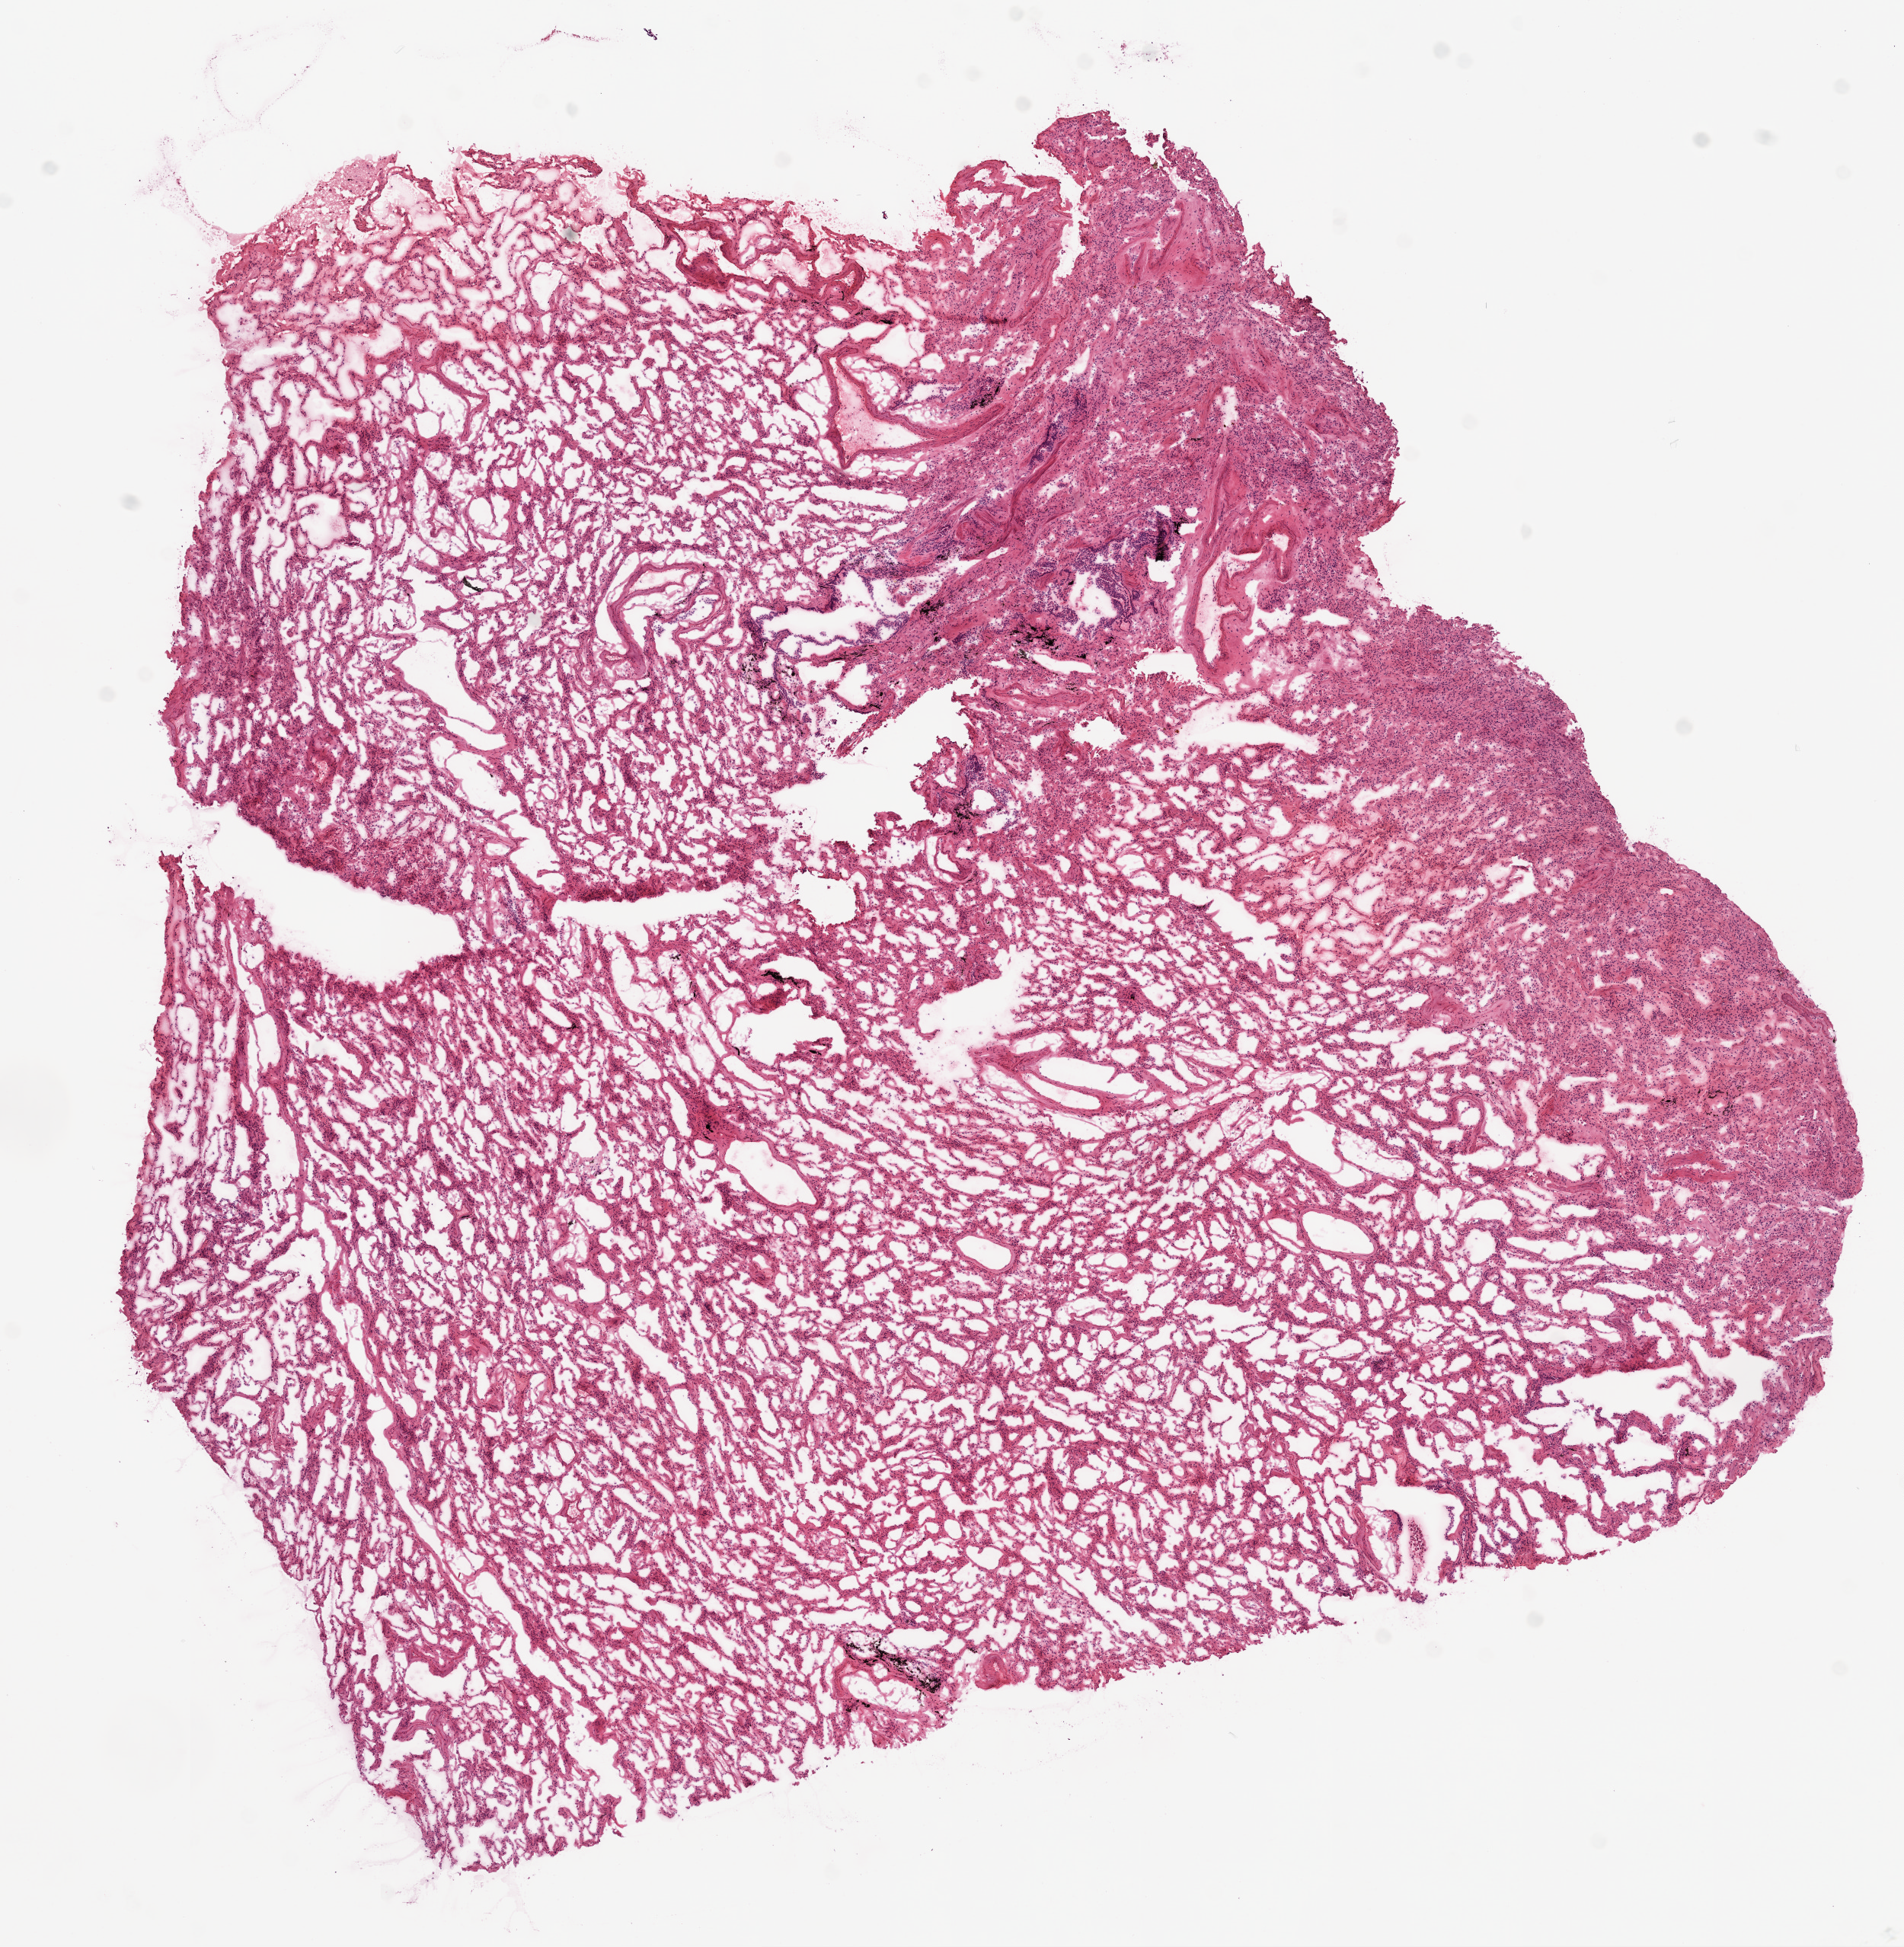
Digitized H&E tissue section (whole slide), shown as a low-resolution overview of the whole scanned area (about 10.0 x 10.3 mm, from a 20x scan); frozen section; solid tissue normal (non-tumour tissue) sample from the lung. Patient: male, age at initial diagnosis 77 years.
This section: solid tissue normal (non-tumour) sample from the same patient. Patient diagnosis: Adenocarcinoma, NOS (upper lobe, lung).